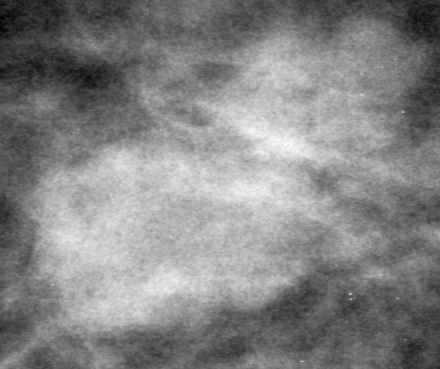
Crop from a digitized film mammogram around one marked abnormality, right breast, CC view.
Finding: mass, shape lobulated, margins obscured; BI-RADS assessment category 0 (incomplete: needs additional imaging); pathology result (as recorded, not read from the image): benign.